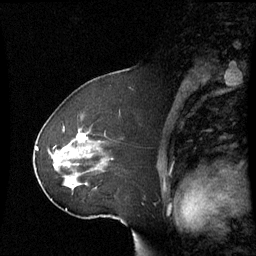
Breast MRI (dynamic contrast-enhanced), one sagittal slice. Dynamic contrast-enhanced series, image 2 of 3 at this slice position (ordered by acquisition). 1.5 T. TE 4.2 ms, TR 8.9 ms. 256 × 256 image matrix, field of view 230 × 230 mm. Female patient, age 51 years. From the clinical record (not read from this slice): setting: breast cancer imaged before/during neoadjuvant chemotherapy; receptor status: HR-positive, HER2-negative.
Annotated regions visible in this slice (semi-automatically segmented with operator editing):
- analysis volume of interest (the breast-tissue region the enhancement analysis was run in; not a lesion): bounding box [x1, y1, x2, y2] px = [42, 123, 108, 199]
- tumour enhancement mask (voxels above the 70 % enhancement threshold inside the analysis volume of interest): [77, 133, 87, 141]